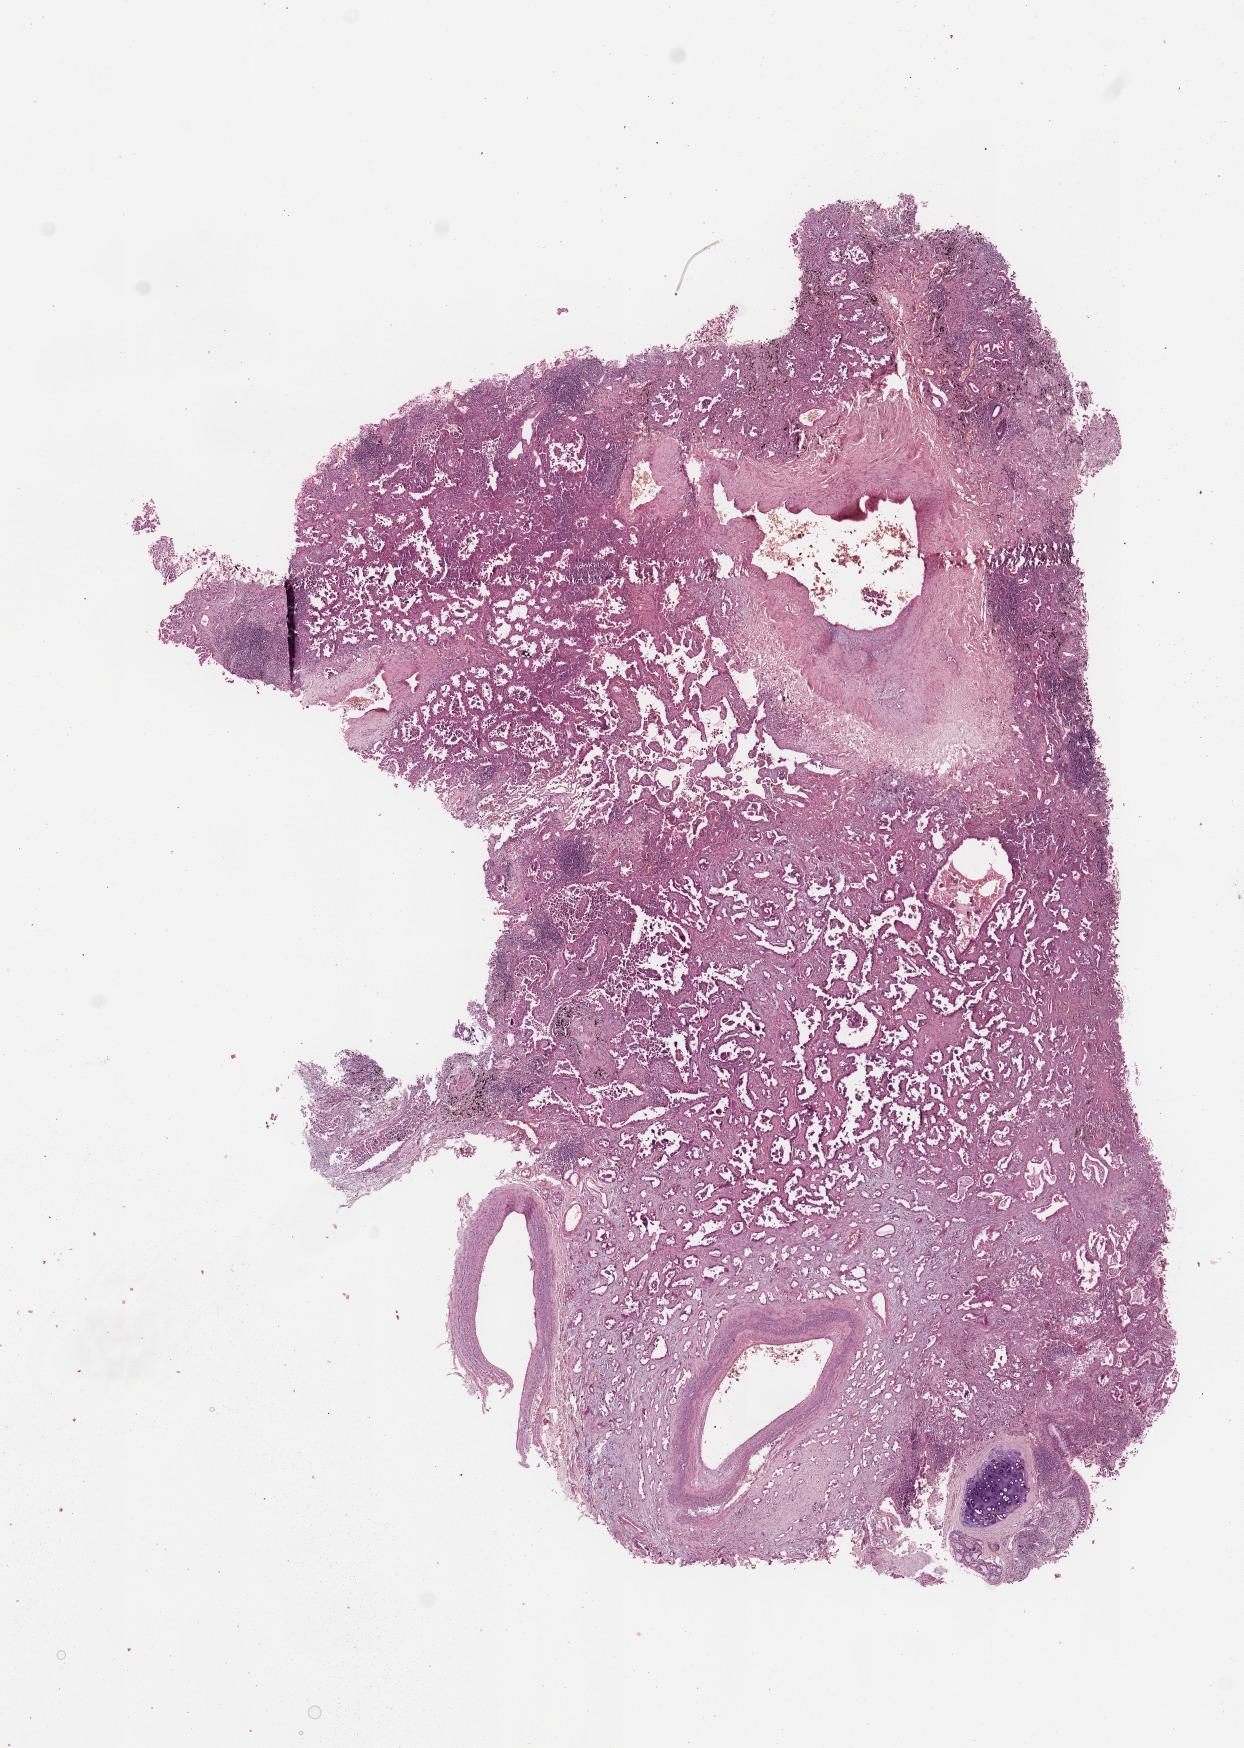
H&E-stained whole-slide image — shown as a low-resolution overview of the whole scanned area (about 9.8 x 13.8 mm, acquisition: 20x scan). Tumour tissue sample, sampled site: lung. 56-year-old male patient. Histologic grade: G2 (moderately differentiated). Slide review estimates, as recorded: tumour nuclei 65%, necrosis 5%.
AJCC pathologic stage: IIIA. Primary tumour site (as recorded): left upper lobe. Histologic diagnosis: Adenocarcinoma, NOS.